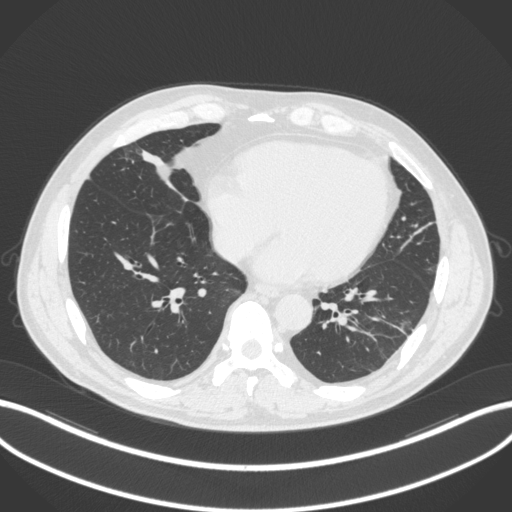
Chest CT, one axial slice; position 88 of 399 along the scan axis; reconstruction kernel B31f; lung window (W 1500 / L -600 HU); 512 × 512 image matrix, field of view 400 × 400 mm. Male patient, age 59 years. From the clinical record (not read from this slice): clinical TNM (as recorded): T2a N1 M0.
Structures marked on this image (bounding box drawn by a radiologist):
- lung tumour (recorded histology: adenocarcinoma): bounding box [x1, y1, x2, y2] px = [137, 141, 180, 178]